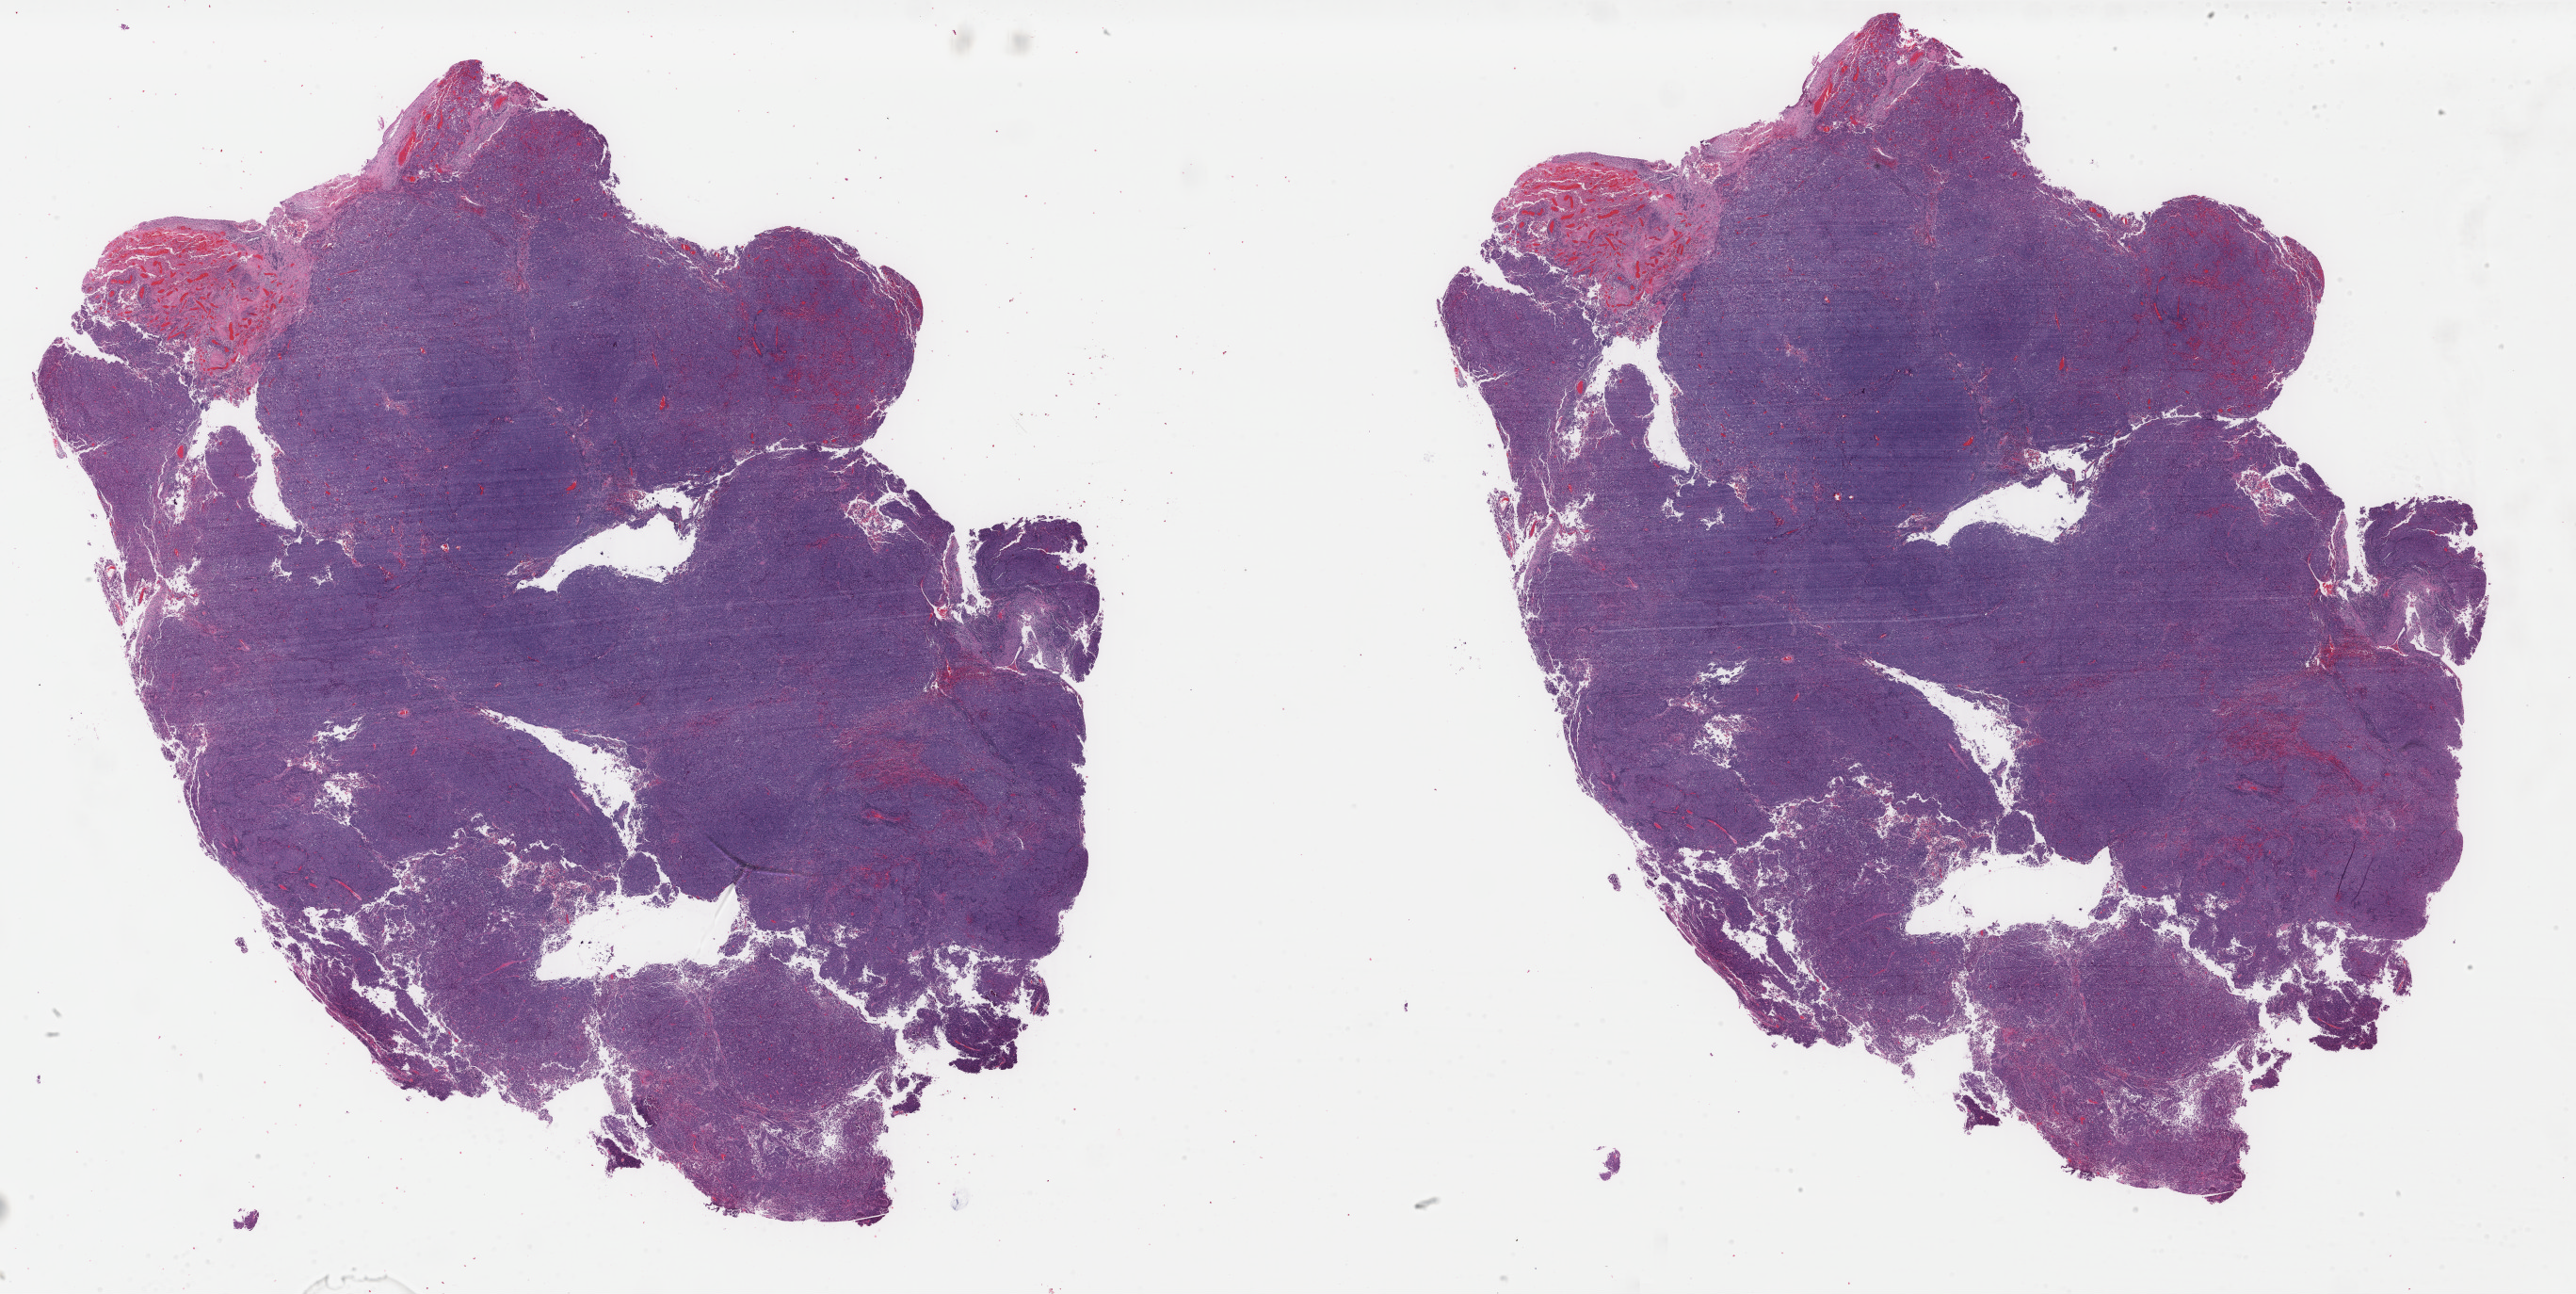
Digitized Hematoxylin and eosin (H&E) stained tissue section (whole slide), a low-resolution overview of the entire scanned area, about 43.4 x 21.8 mm (slide scanned at 40x). FFPE section. Uterus, primary tumour sample. Female, age 62 years at initial diagnosis. Histologic grade: G3 (poorly differentiated).
Histologic diagnosis: Endometrioid adenocarcinoma, NOS (endometrium). FIGO stage: IB.